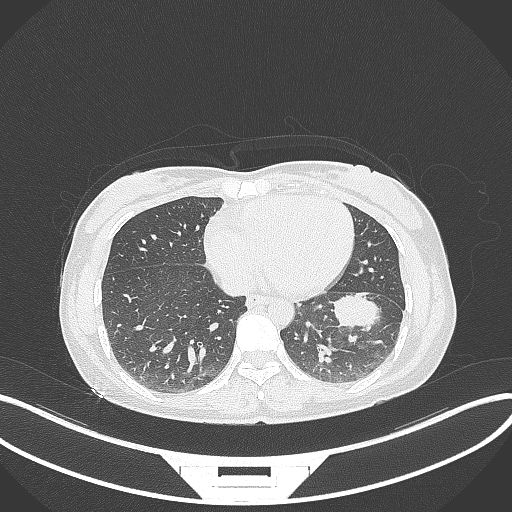
Chest CT, one axial slice. Lung window (W 1500 / L -600 HU). 512 × 512 image matrix. Female patient, age 41 years. Case-level facts recorded for this patient, not image findings: clinical TNM (as recorded): T2a N3 M1b.
Outlined on this slice (rectangle marked by the reading radiologist):
- lung tumour (recorded histology: adenocarcinoma): box from (x=330, y=290) to (x=388, y=333) px